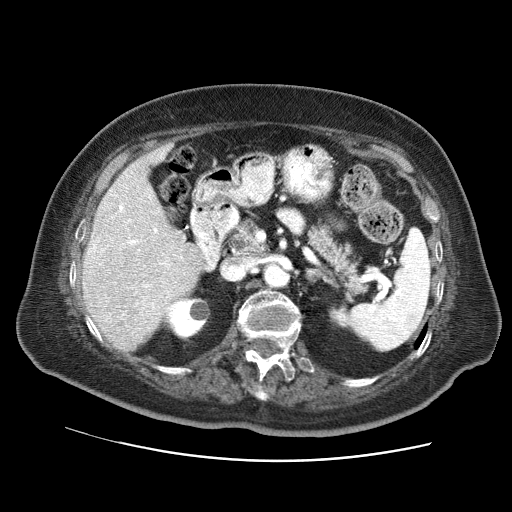
Contrast-enhanced abdominal CT (liver protocol), one axial slice. Slice 34 of 73 in the series (ordered by position). Reconstruction kernel STANDARD. Soft-tissue window (W 400 / L 40 HU). 2.5 mm slice thickness. 512 × 512 image matrix, field of view 380 × 380 mm. Case-level facts recorded for this patient, not image findings: diagnosis: hepatocellular carcinoma (patient treated with transarterial chemoembolisation; whether this scan precedes or follows treatment is not stated here); TNM stage (as recorded): Stage-I; Child-Pugh class: A; tumour differentiation: well differentiated.
Annotated regions visible in this slice (semi-automatic segmentation, software-assisted and operator-edited):
- liver parenchyma outside the tumour (the mass and vessels are separate outlines, so this box may not span the whole liver): bounding box [x1, y1, x2, y2] px = [82, 145, 202, 350]
- liver vessels: [88, 153, 170, 315]